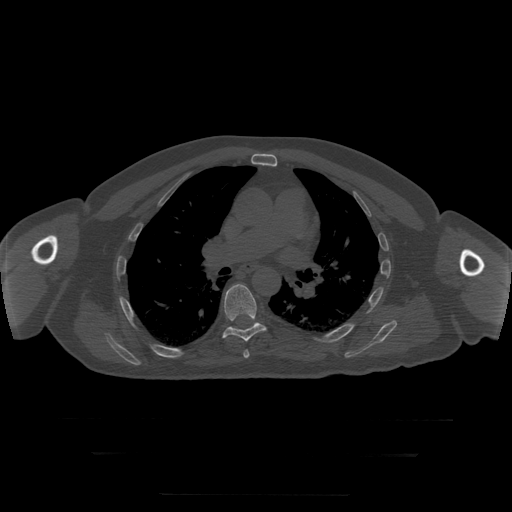
CT including the spine, one axial slice; slice 188 of 397 in the series (ordered by position); bone window (W 1800 / L 400 HU); 1.25 mm slice thickness; 512 × 512 image matrix, field of view 510 × 510 mm. Patient age 73 years. From the clinical record (not read from this slice): primary cancer: prostate.
Structures marked on this image (semi-automatic segmentation, software-assisted and operator-edited):
- T6 vertebra: bounding box <244,351,250,359> (left, top, right, bottom; pixels)
- T7 vertebra: <223,284,267,342>
- T8 vertebra: <250,326,254,329>